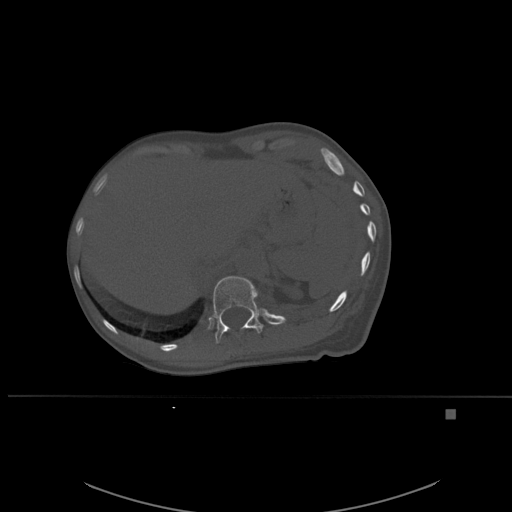
CT including the spine, one axial slice. Position 283 of 537 along the scan axis. Bone window (W 1800 / L 400 HU). 1.5 mm slice thickness. 512 × 512 image matrix. Female patient, age 45 years. Case-level facts recorded for this patient, not image findings: primary cancer: lung.
Outlined on this slice (semi-automatic segmentation, software-assisted and operator-edited):
- T12 vertebra: bounding box (x1, y1, x2, y2) in pixels: (213, 276, 264, 344)